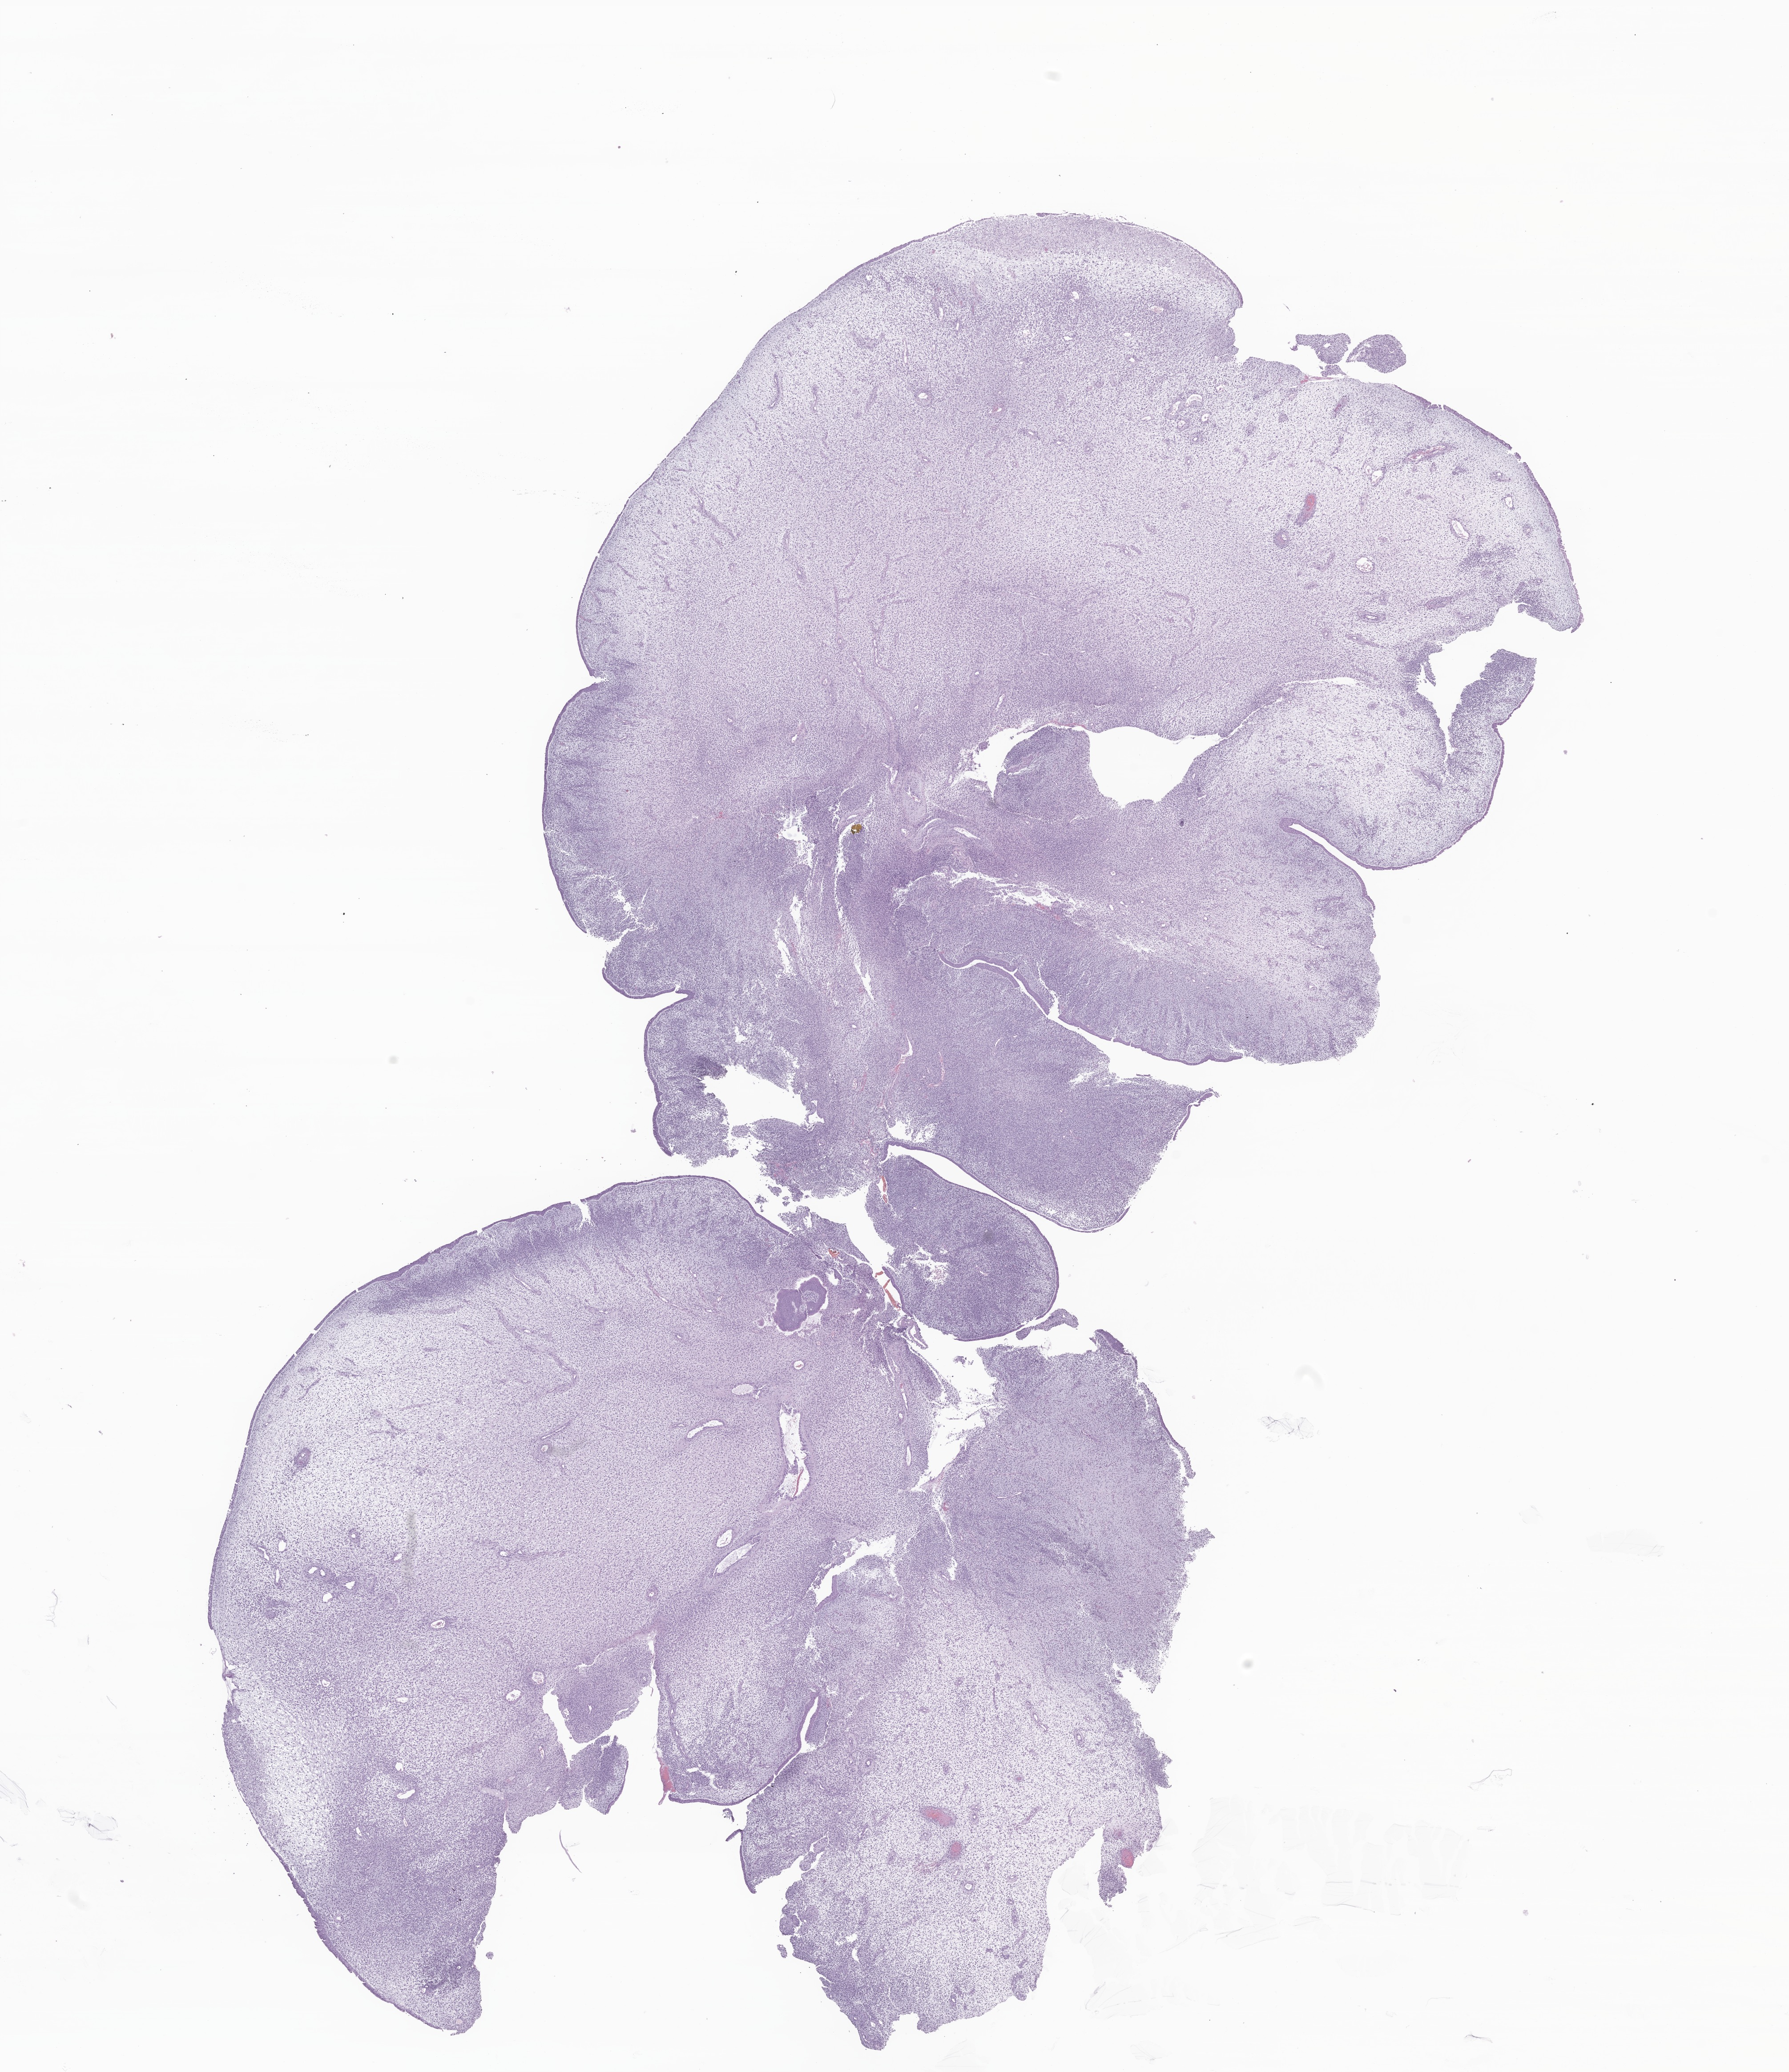
Digitized haematoxylin and eosin-stained section of tumor tissue from the urinary bladder, a low-resolution overview of the entire scanned area, about 17.0 x 19.6 mm. Formalin-fixed, paraffin-embedded (FFPE) tissue. Patient male; age 768 days (about 2.1 years).
Diagnosis (ICD-O-3 morphology term): Embryonal rhabdomyosarcoma, NOS.